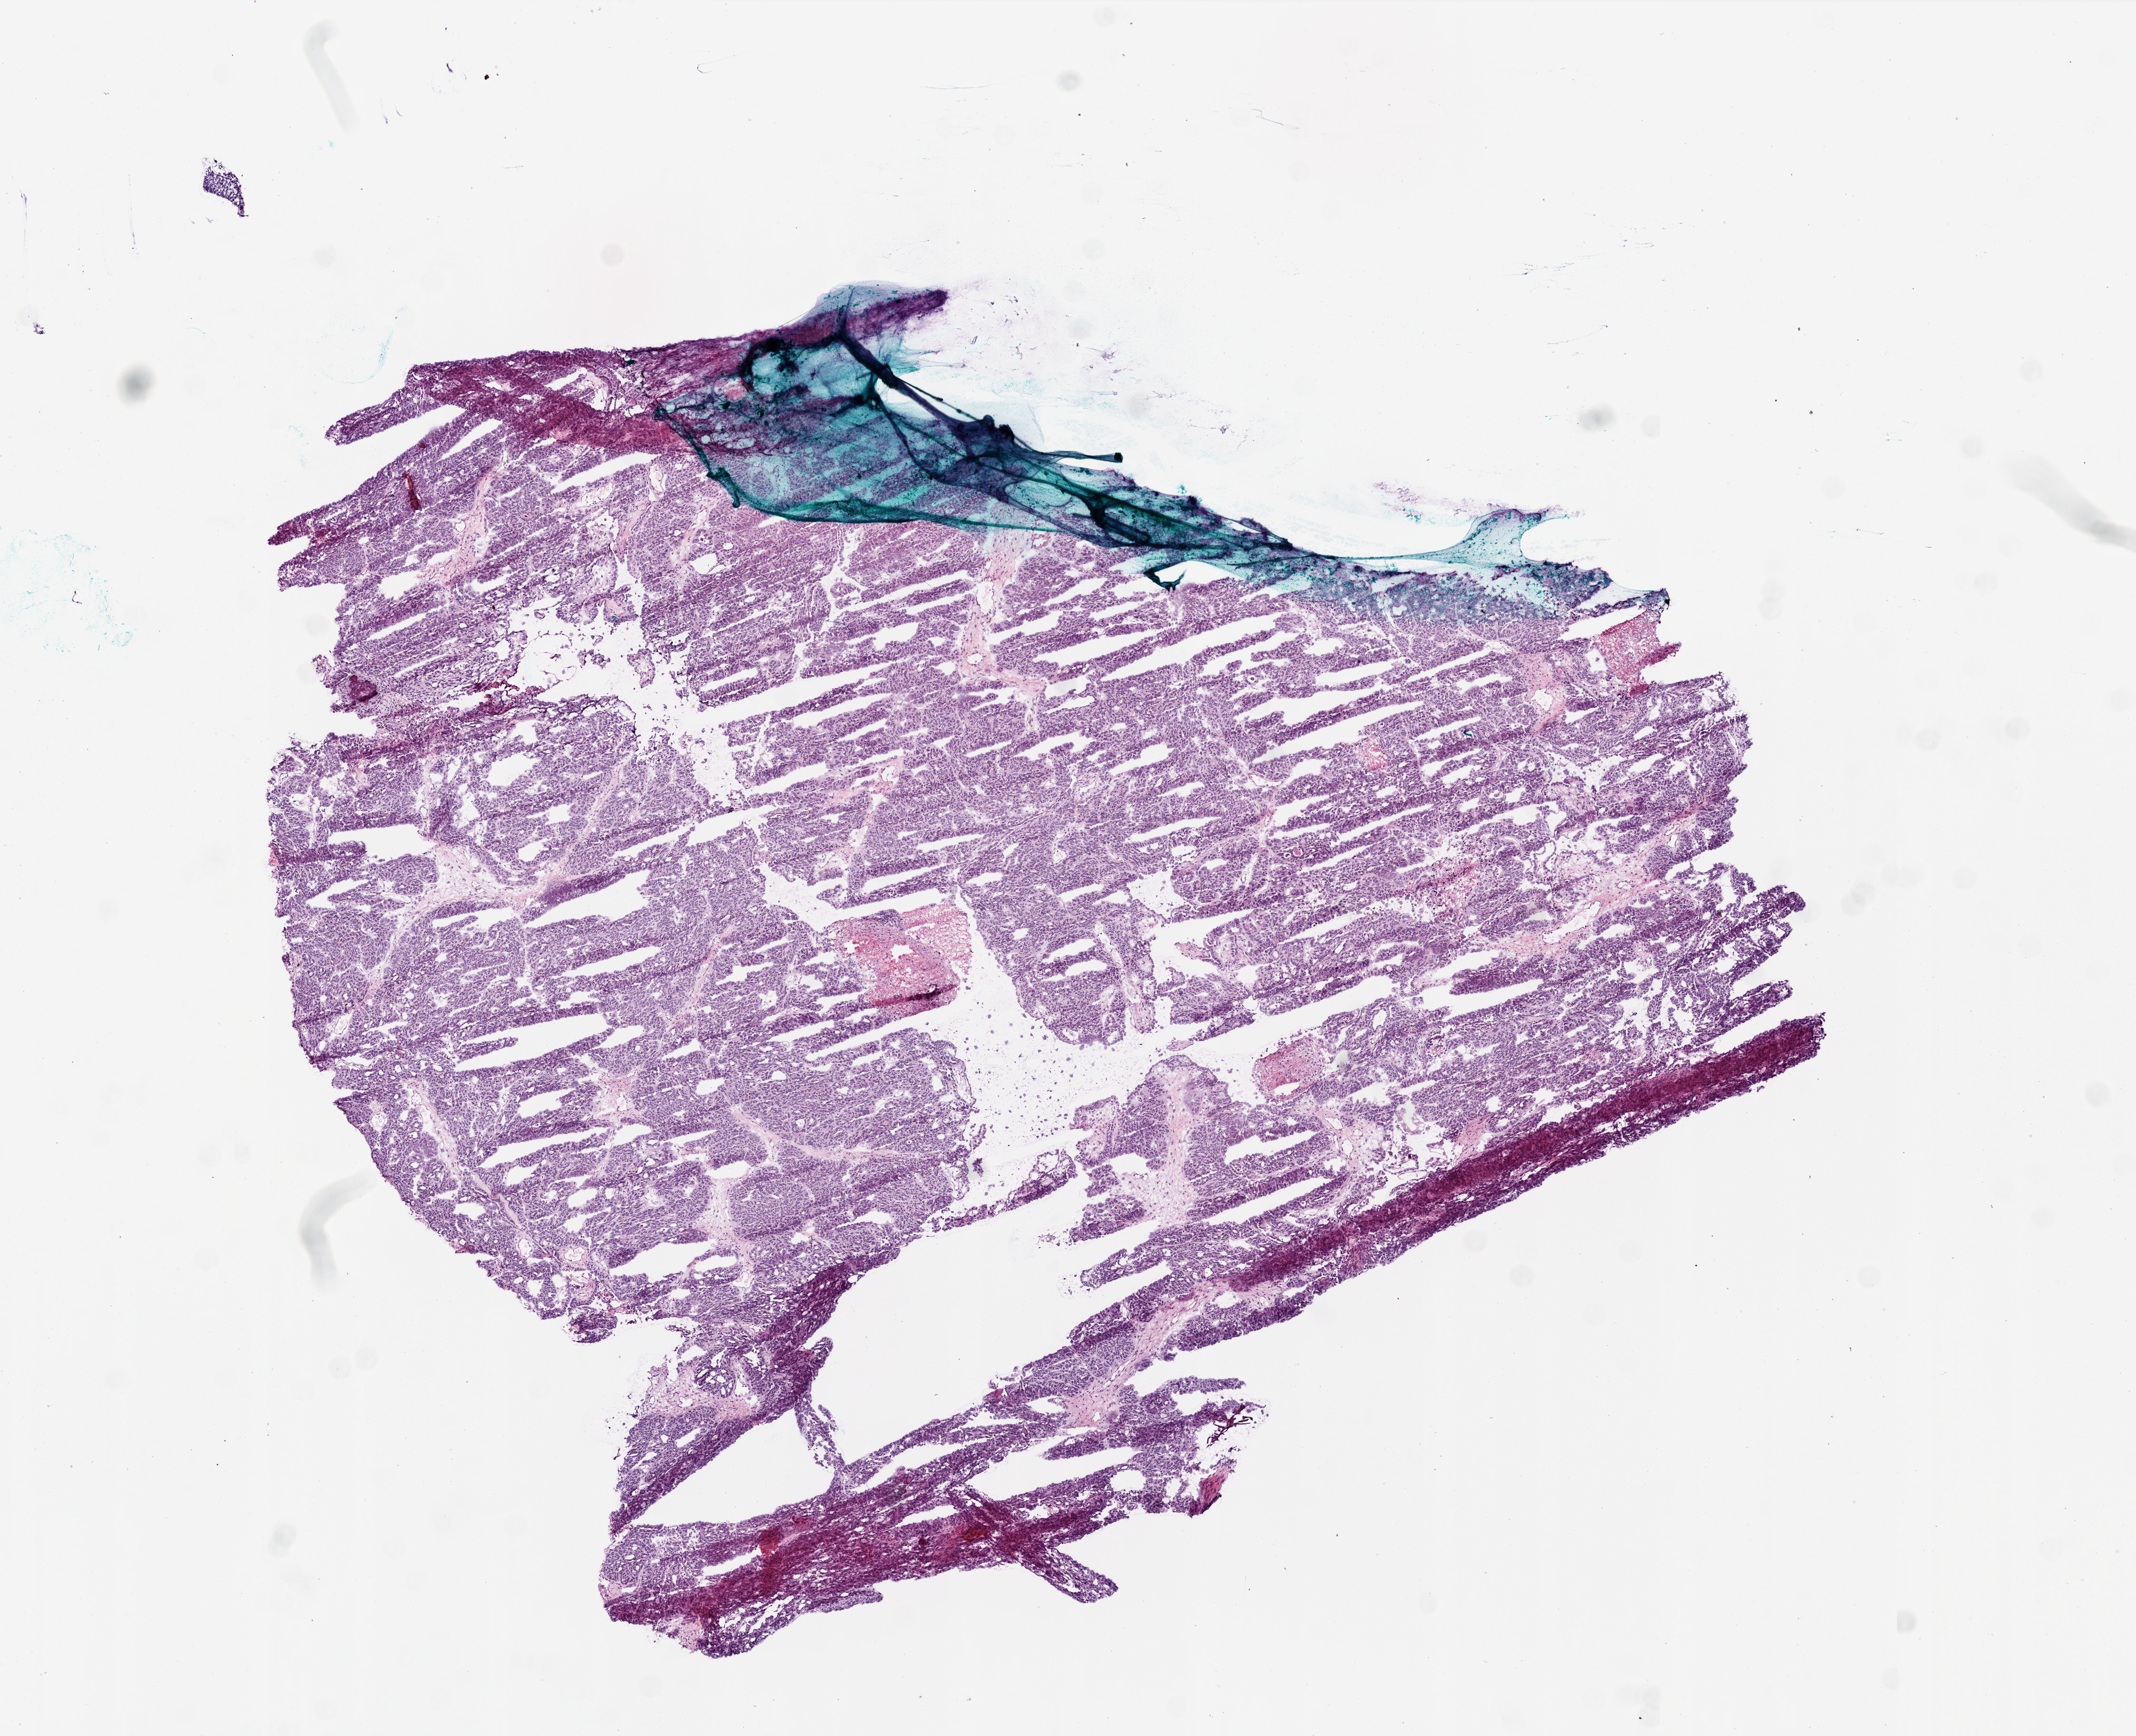
Digitized H&E-stained tissue section (whole slide) — low-resolution overview of the scanned area, about 9.0 x 7.3 mm (acquisition: 20x scan). Frozen section. Ovary, primary tumour sample. Female patient; age at initial diagnosis 70 years. Histologic grade: G3 (poorly differentiated). Slide review estimates, as recorded: tumour cells 95%, tumour nuclei 98%, normal cells 0%, stromal cells 5%, necrosis 0%.
FIGO stage: IIIC. Pathologic diagnosis: Serous cystadenocarcinoma, NOS.